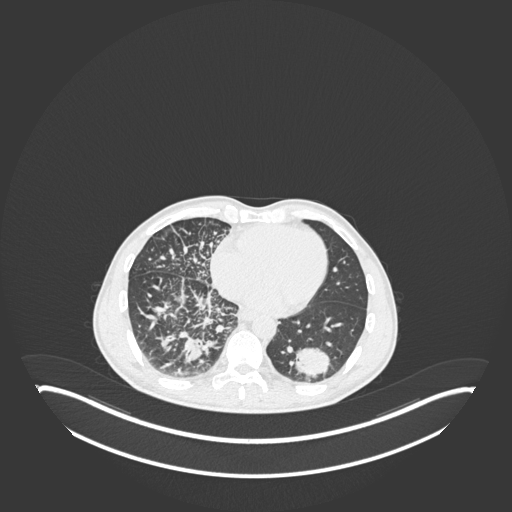
Chest CT, one axial slice. Slice 77 of 237 in the series (ordered by position). Reconstruction kernel B30f. 120 kVp. Lung window (W 1500 / L -600 HU). 1 mm slice thickness. 512 × 512 image matrix, field of view 500 × 500 mm. Male patient, age 49 years. Case-level facts recorded for this patient, not image findings: clinical TNM (as recorded): T2b N1 M0.
Structures marked on this image (bounding box drawn by a radiologist):
- lung tumour (recorded histology: adenocarcinoma): bounding box <290,344,333,382> (left, top, right, bottom; pixels)